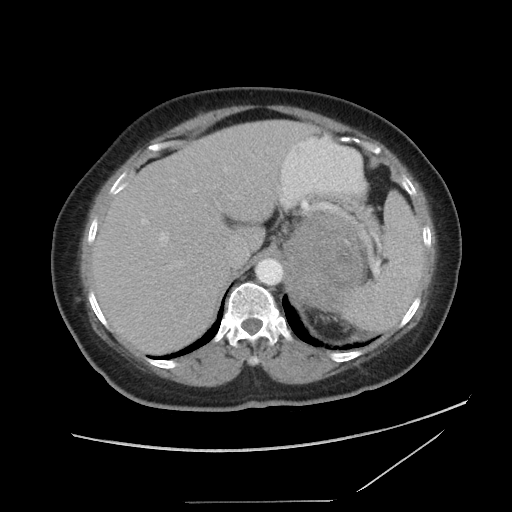
Contrast-enhanced abdominal CT, one axial slice. Slice 65 of 86 in the series (ordered by position). Reconstruction kernel STANDARD. 120 kVp. Soft-tissue window (W 400 / L 40 HU). 5 mm slice thickness. 512 × 512 image matrix. Female patient, age 77 years. From the clinical record (not read from this slice): diagnosis: adrenocortical carcinoma; tumour side: left adrenal.
Annotated regions visible in this slice (semi-automatic segmentation, software-assisted and operator-edited):
- mass: box from (x=285, y=214) to (x=366, y=311) px